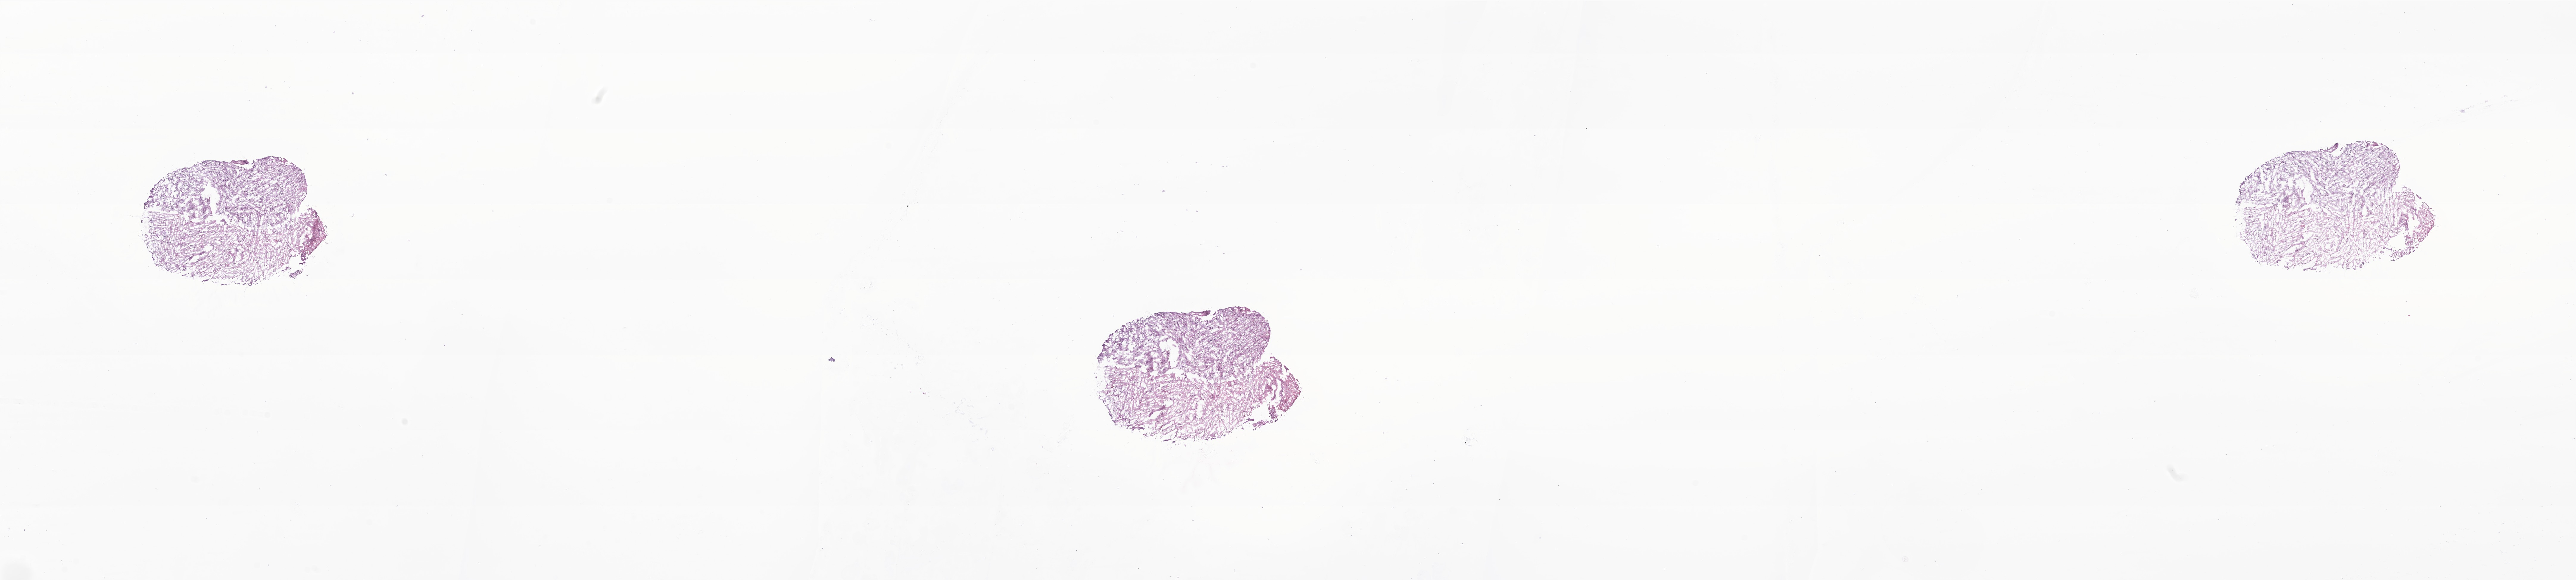
Whole-slide image, haematoxylin and eosin stain of tumor tissue from the cerebellum — whole scanned area (about 36.5 x 8.2 mm) shown as a low-resolution overview. Cryosection (OCT / tissue freezing medium). Patient: male, age 195 months (16 years 3 months).
Recorded diagnosis: Pilocytic astrocytoma.